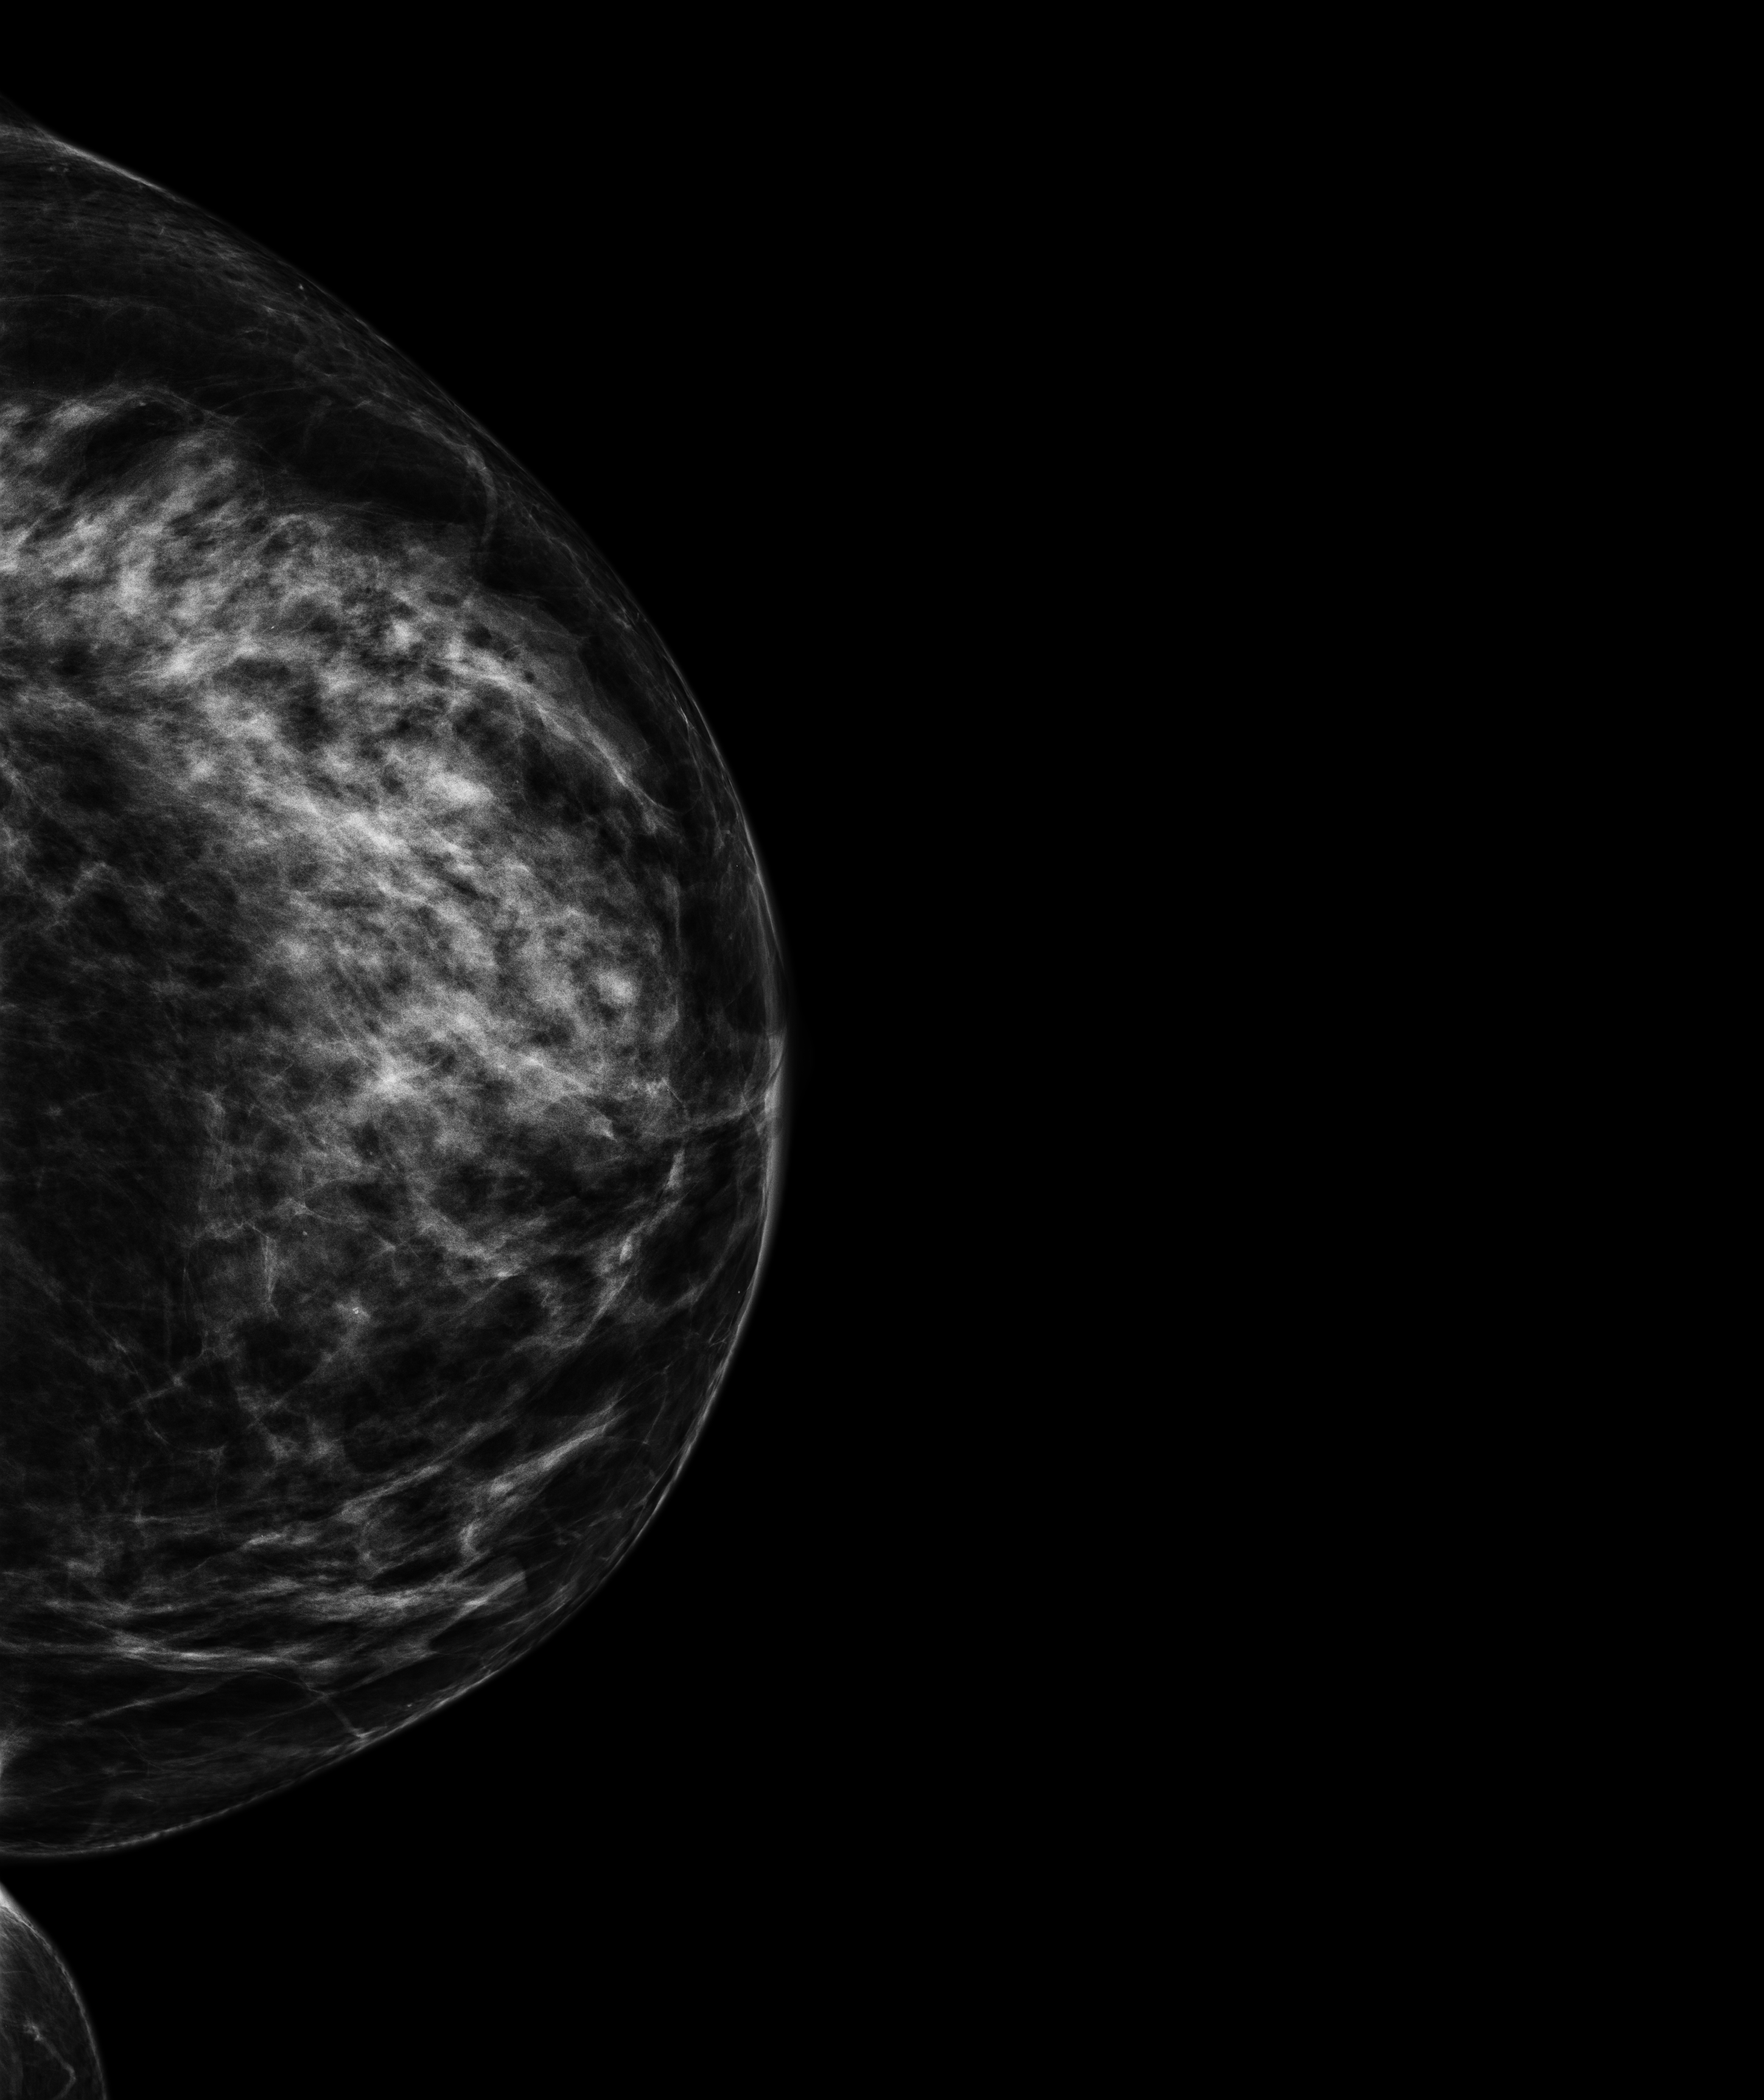
Annual screening mammography examination, system: Senographe Pristina. Female patient, age 65 years.
Image type: full-field digital mammogram. Breast: left. Projection: craniocaudal (CC) view.